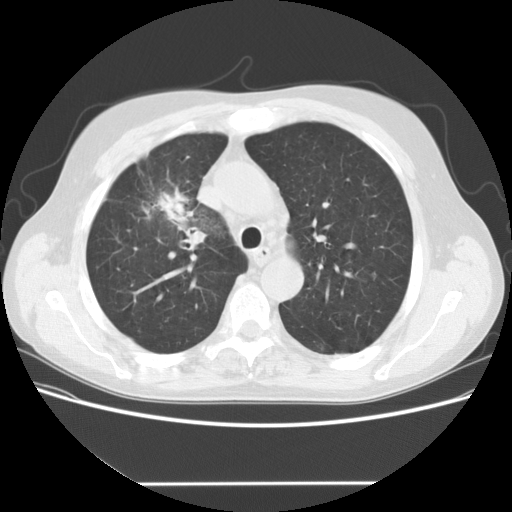
Chest CT (low-dose screening protocol), one axial image; first (baseline) screen; lung window (W 1500 / L -600 HU); 2.5 mm slice thickness; 120 kVp; 512 × 512 image matrix, field of view 360 × 360 mm. Male, age 56 years at enrolment. Current smoker at enrolment.
- Expert reader's lesion annotation, bounding box <126,169,218,250> (left, top, right, bottom; pixels).
- The screening reader recorded 2 non-calcified nodules or masses ≥4 mm on this exam; which of them this box marks is not recorded.